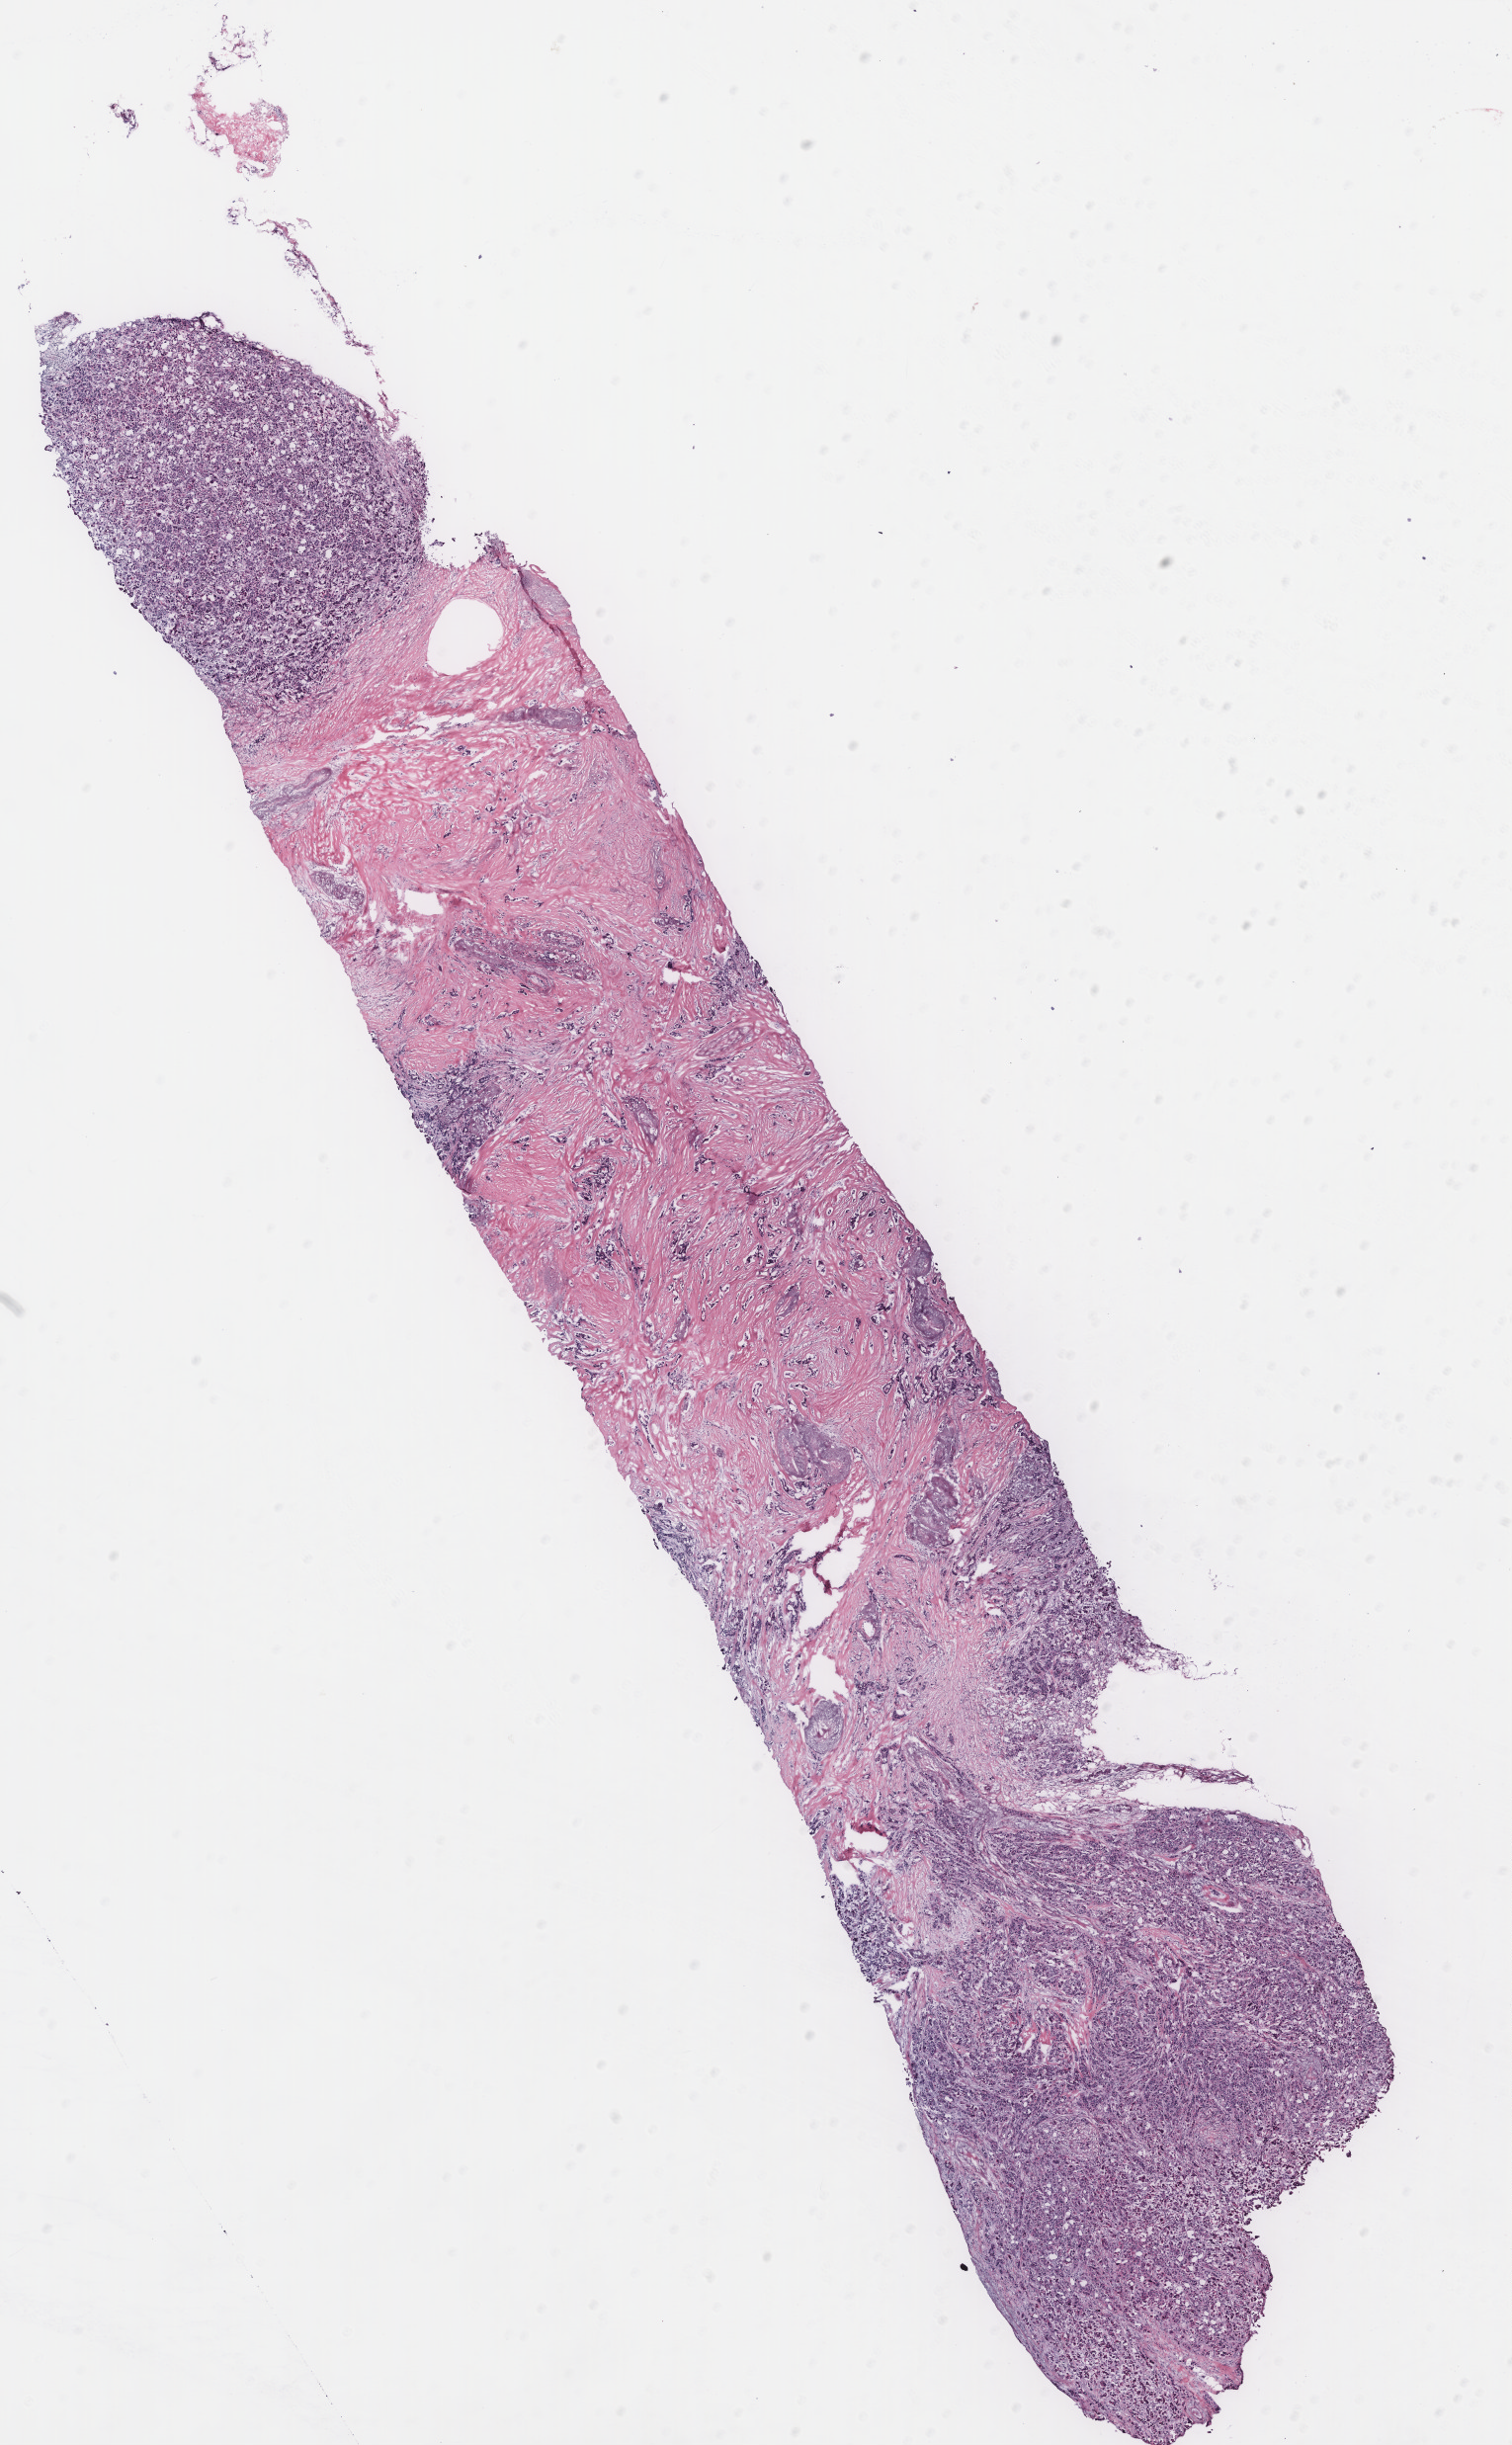
Digitized H&E-stained tissue section (whole slide) — a low-resolution overview of the entire scanned area, about 12.2 x 19.8 mm (from a 40x scan), breast, tissue type not recorded. Patient: female, age 88 years.
• patient diagnosis: Infiltrating duct carcinoma, NOS